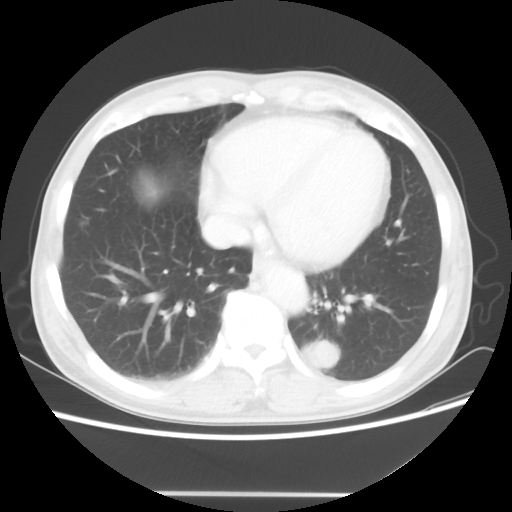
Chest CT, one axial slice. Position 18 of 60 along the scan axis. Reconstruction kernel STANDARD. Lung window (W 1500 / L -600 HU). 5 mm slice thickness. 512 × 512 image matrix, field of view 360 × 360 mm. Male patient, age 55 years. From the clinical record (not read from this slice): clinical TNM (as recorded): T1c N3 M0; histopathological grade: G3.
Annotated regions visible in this slice (rectangle marked by the reading radiologist):
- lung tumour (recorded histology: small cell carcinoma): bounding box (x1, y1, x2, y2) in pixels: (301, 336, 342, 372)